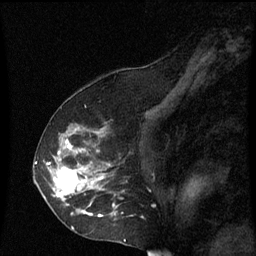
Breast MRI (dynamic contrast-enhanced), one sagittal slice; slice 39 of 60 in the series (ordered by position); dynamic contrast-enhanced series, image 2 of 3 at this slice position (ordered by acquisition); 1.5 T; TE 4.2 ms, TR 8.9 ms; 2 mm slice thickness; 256 × 256 image matrix. Female patient, age 53 years. Case-level facts recorded for this patient, not image findings: setting: breast cancer imaged before/during neoadjuvant chemotherapy; receptor status: HR-positive, HER2-negative.
Annotated regions visible in this slice (semi-automatic segmentation, software-assisted and operator-edited):
- analysis volume of interest (the breast-tissue region the enhancement analysis was run in; not a lesion): bounding box (x1, y1, x2, y2) in pixels: (38, 128, 123, 231)
- tumour enhancement mask (voxels above the 70 % enhancement threshold inside the analysis volume of interest): (46, 140, 119, 217)